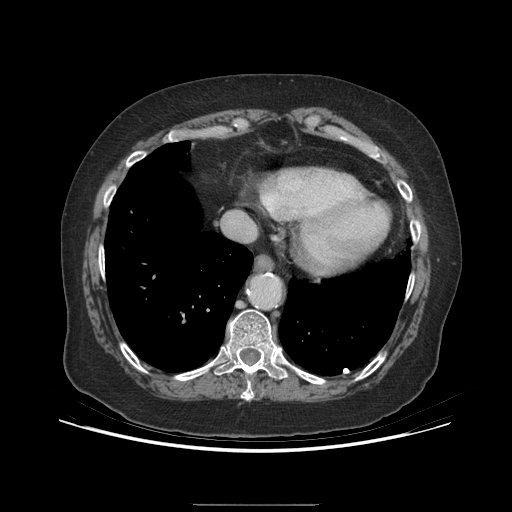
Contrast-enhanced abdominal CT (liver protocol), one axial slice; slice 183 of 192 in the series (ordered by position); reconstruction kernel STANDARD; soft-tissue window (W 400 / L 40 HU); 2.5 mm slice thickness; 512 × 512 image matrix, field of view 400 × 400 mm. Case-level facts recorded for this patient, not image findings: diagnosis: hepatocellular carcinoma (patient treated with transarterial chemoembolisation; whether this scan precedes or follows treatment is not stated here); TNM stage (as recorded): Stage-I; Child-Pugh class: A; tumour differentiation: moderately differentiated; tumour nodularity: uninodular.
Structures marked on this image (semi-automatically segmented with operator editing):
- abdominal aorta: bounding box [x1, y1, x2, y2] px = [251, 275, 279, 307]